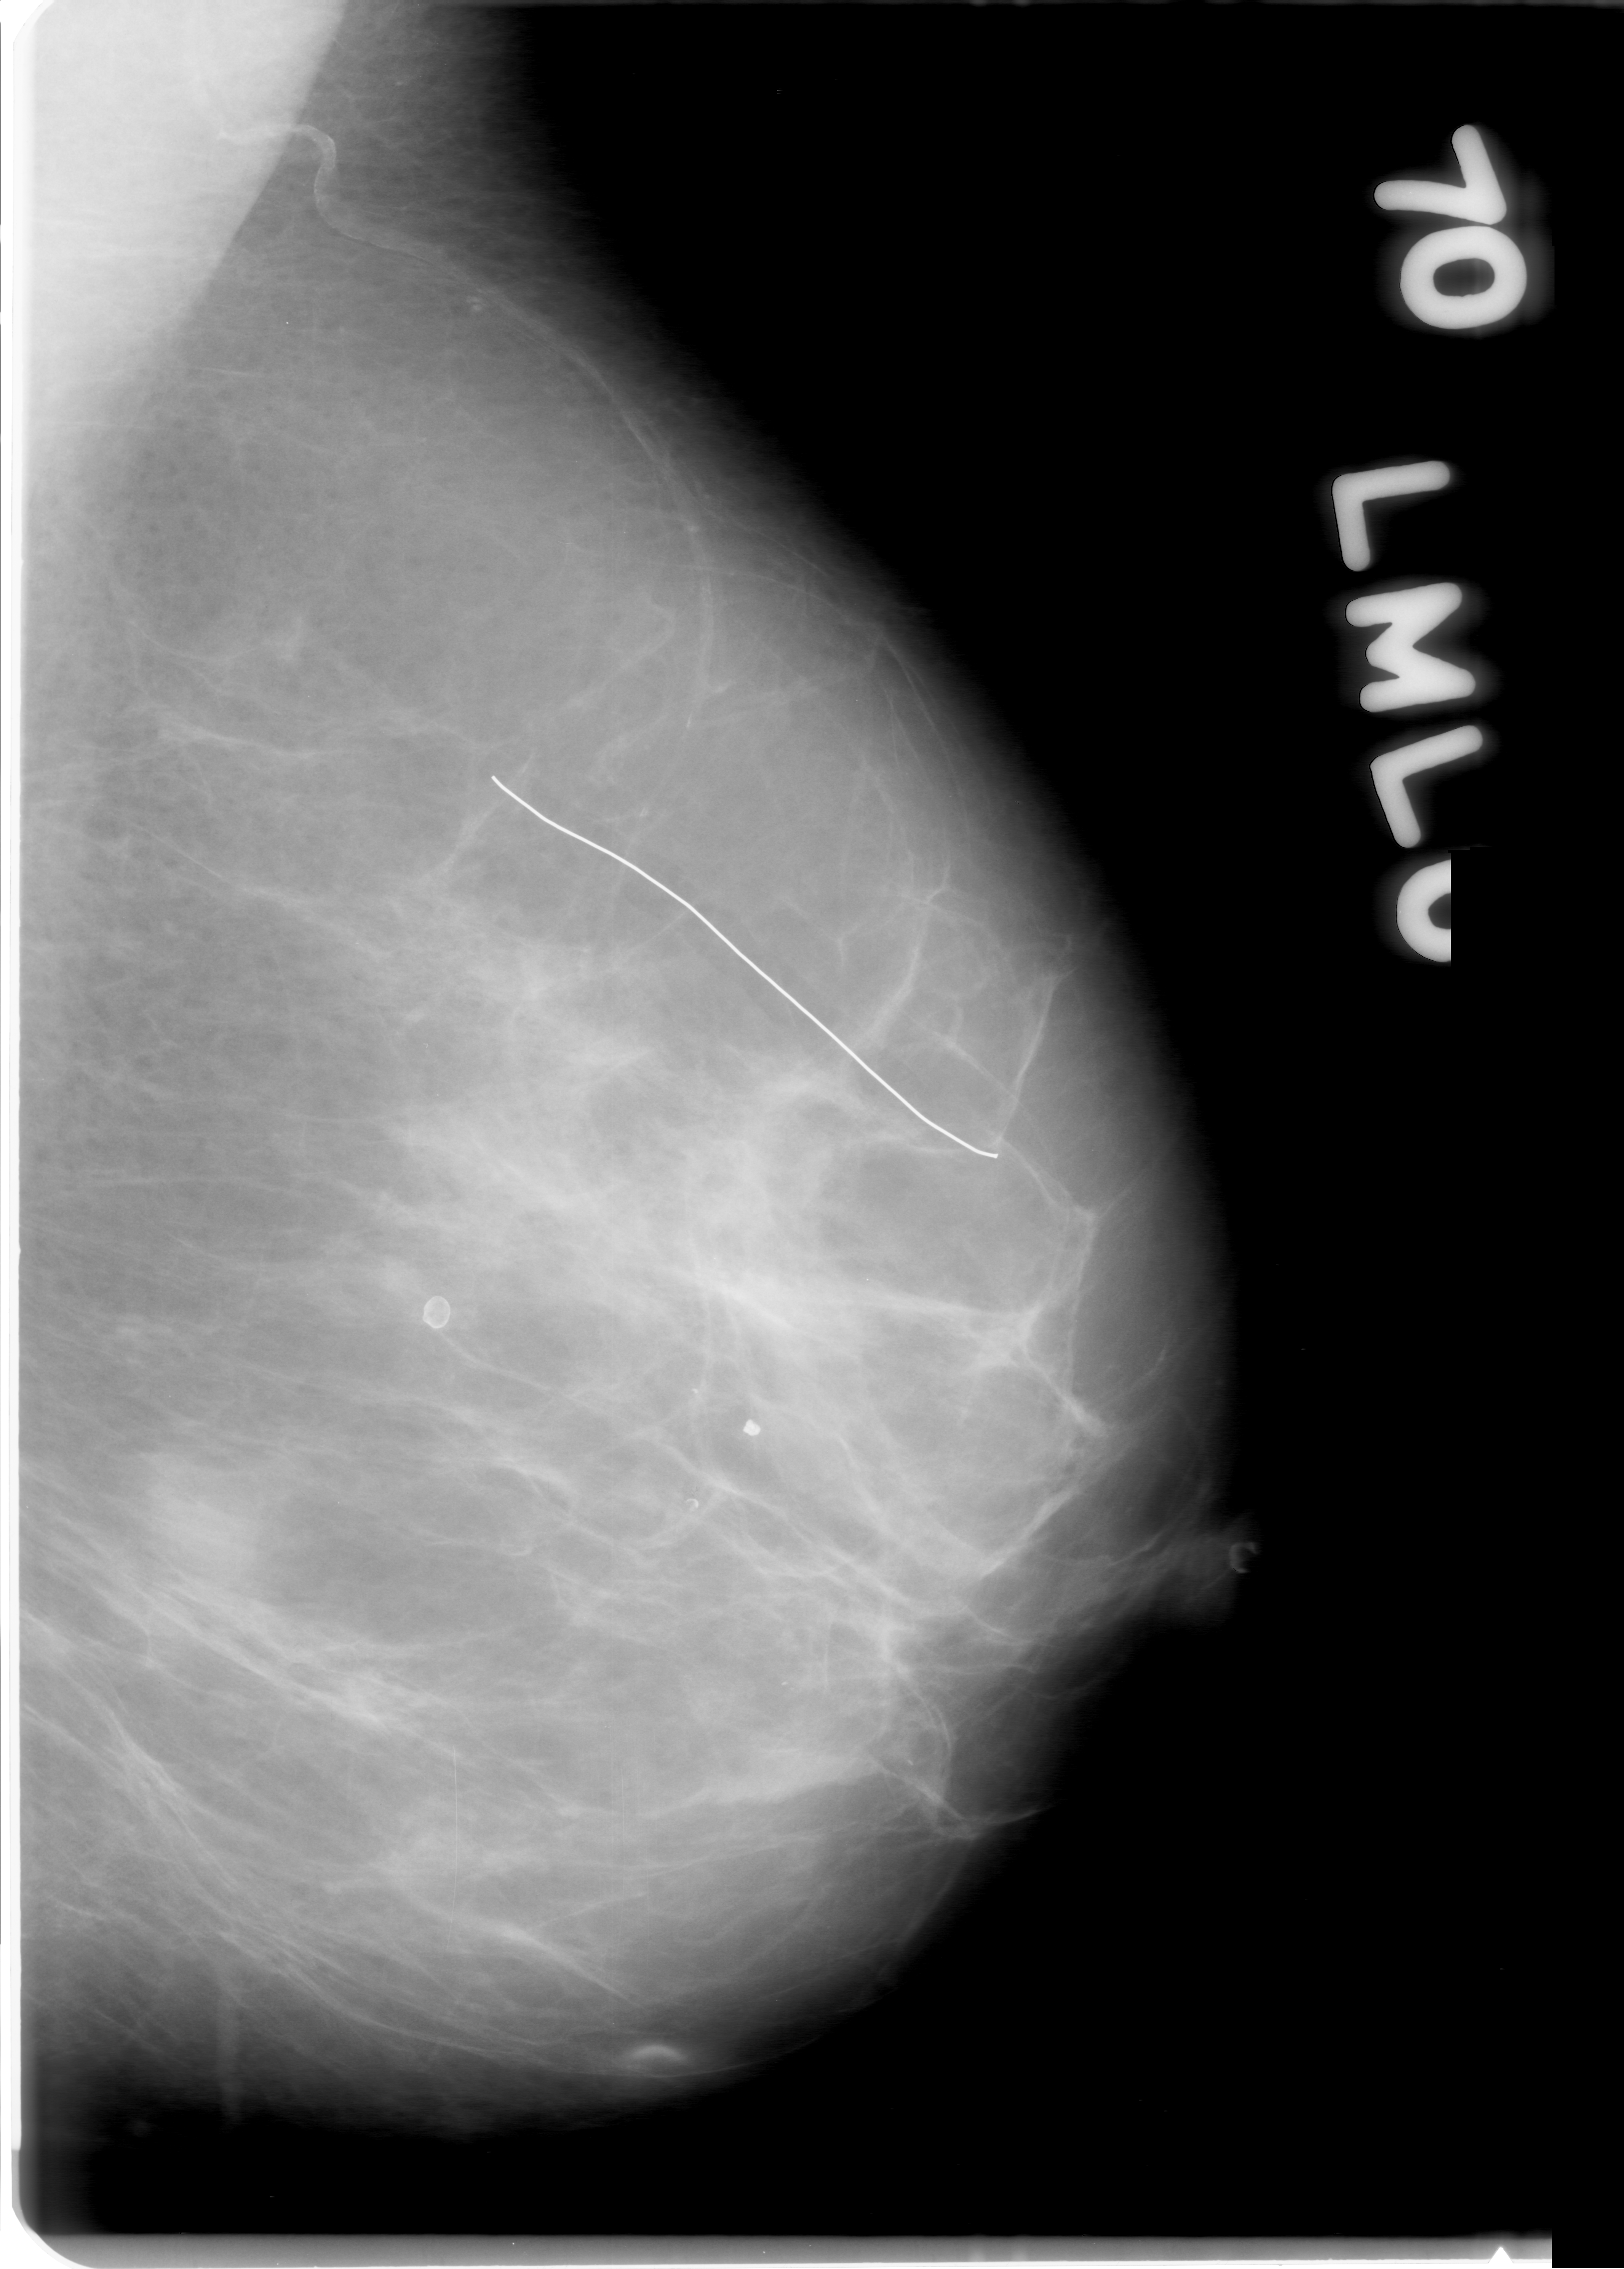
Digitized screen-film mammogram; left breast; MLO view; breast composition: scattered fibroglandular densities (BI-RADS density category 2 of 4).
Radiologist-marked abnormalities on this image: mass, shape oval, margins microlobulated; BI-RADS assessment category 0 (incomplete: needs additional imaging); subtlety rating 5 on a 1 (subtle) to 5 (obvious) scale; pathology (as recorded): benign.